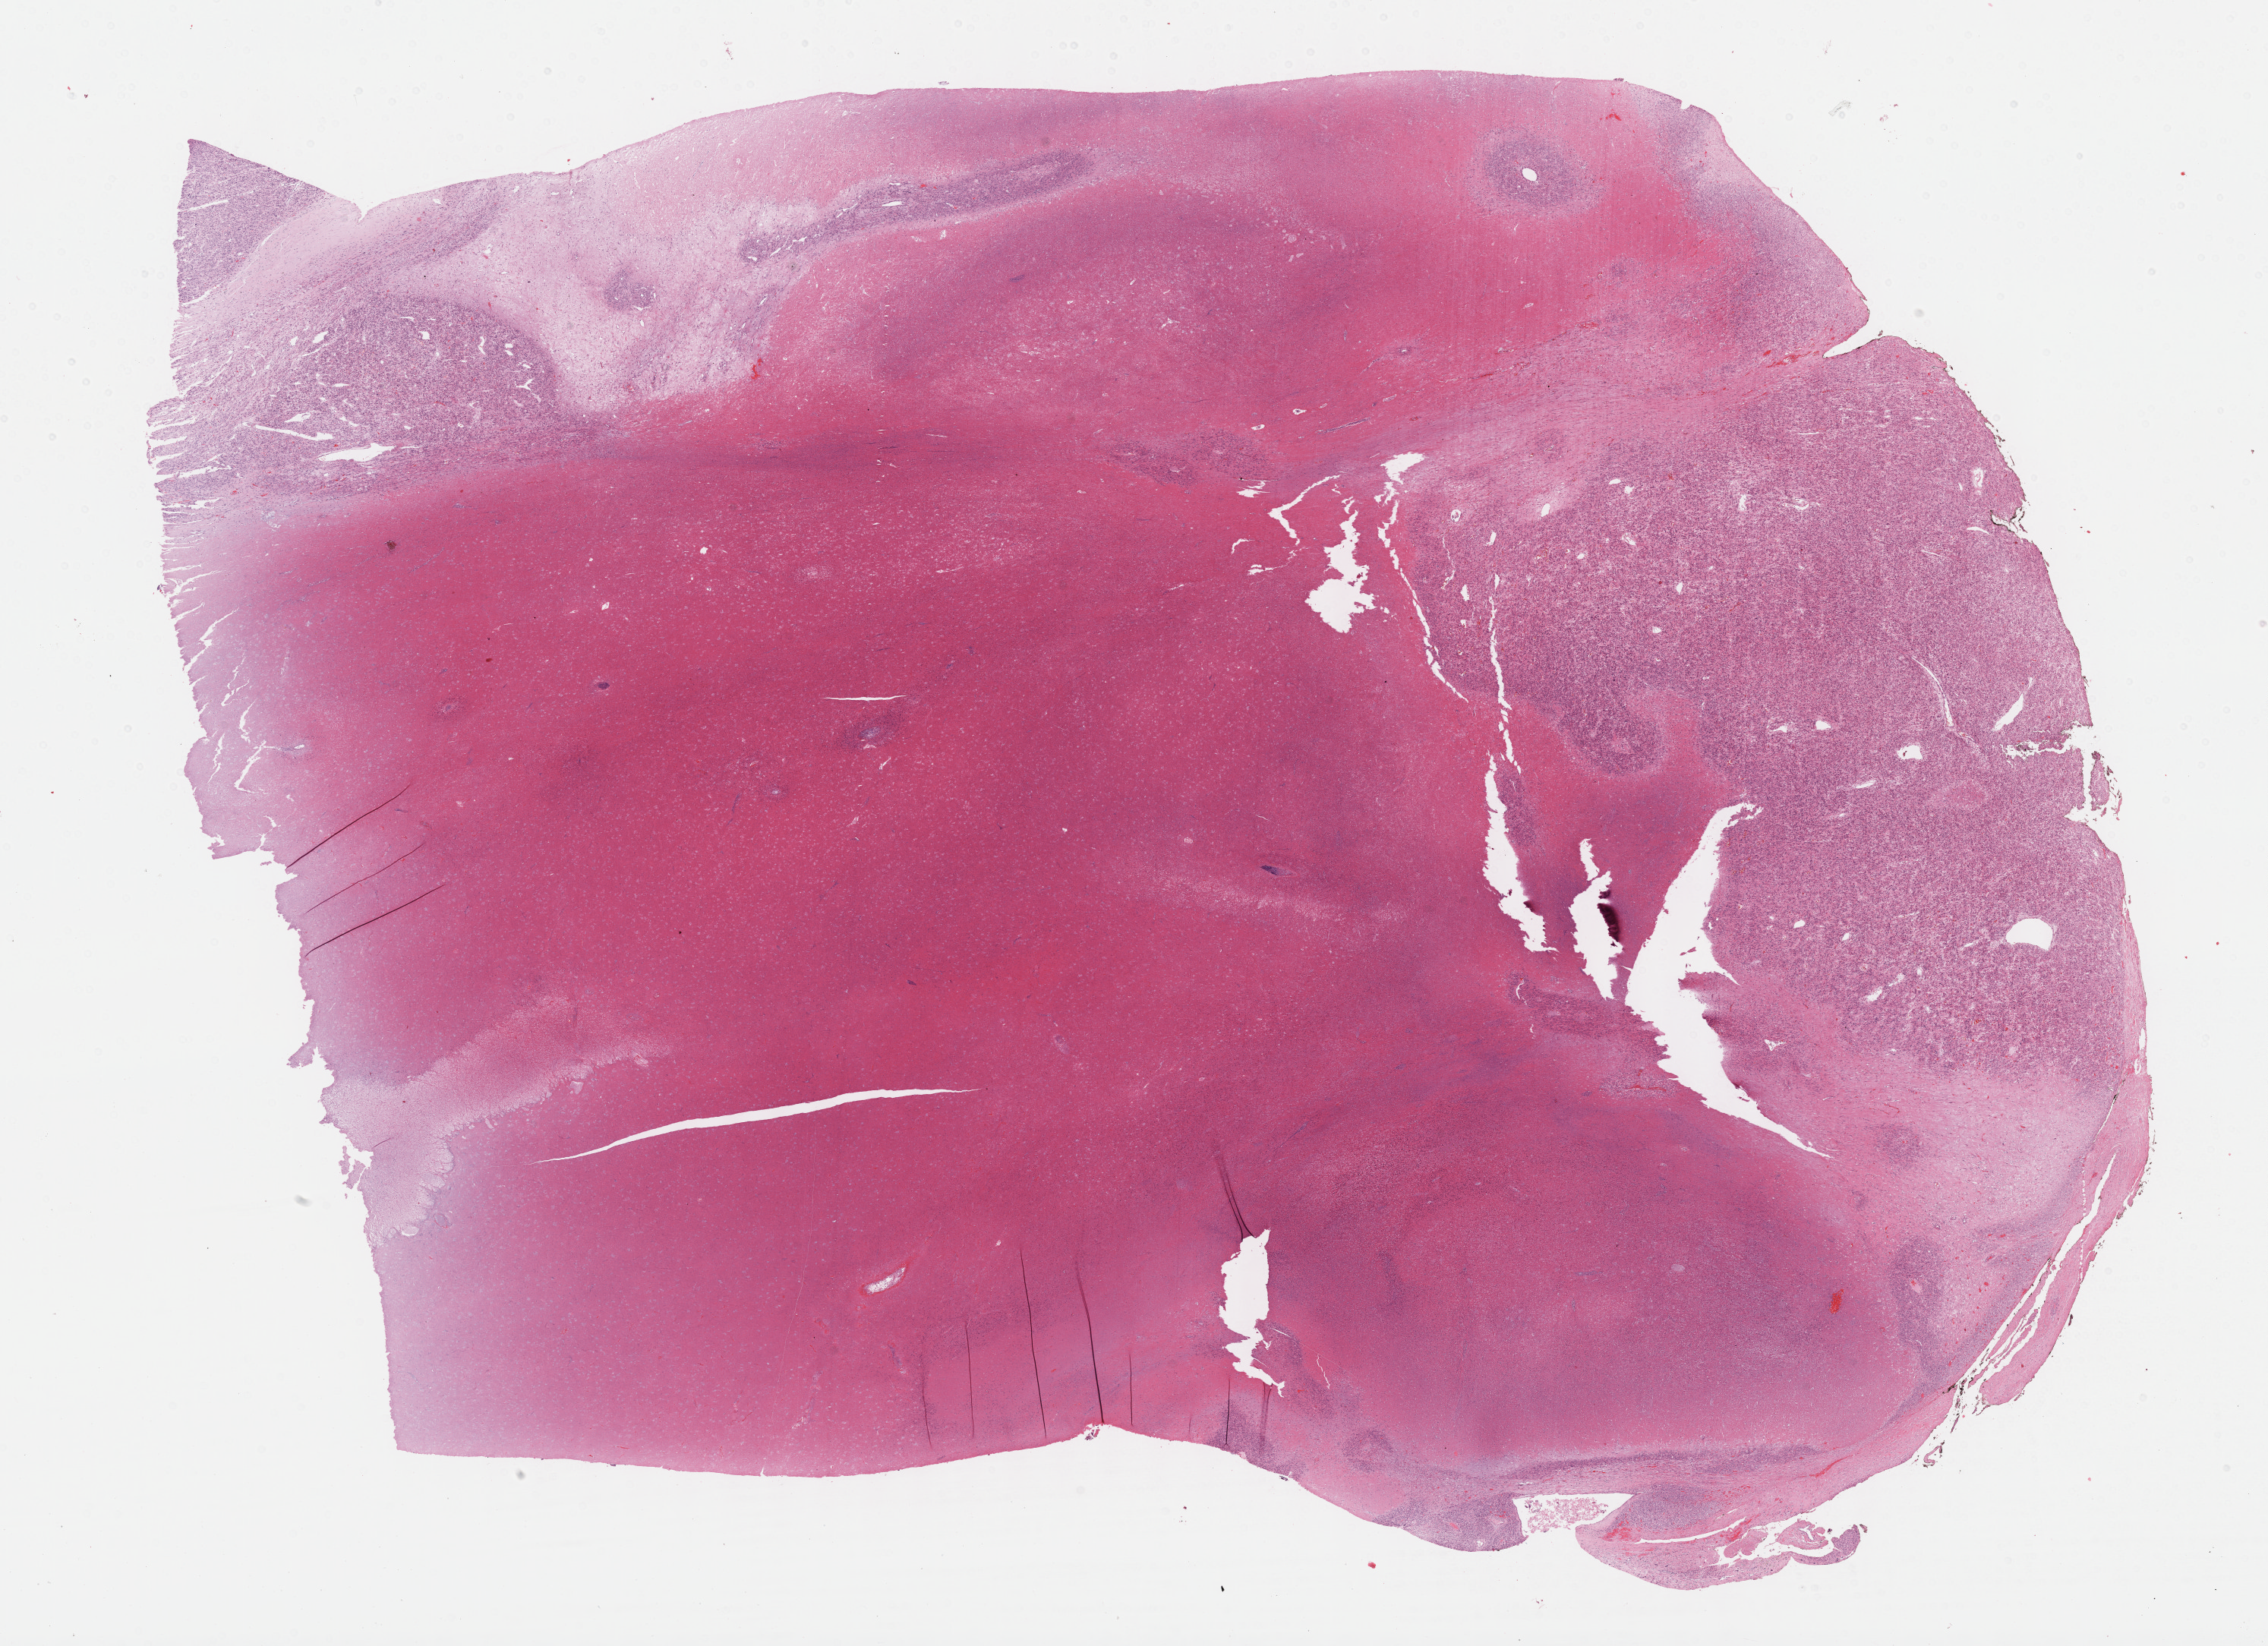
H&E whole-slide image — low-resolution overview of the scanned area, about 24.2 x 17.5 mm. FFPE section. Retroperitoneum and peritoneum, primary tumour sample. Female patient; age at initial diagnosis 53 years.
Pathologic diagnosis: Leiomyosarcoma, NOS (retroperitoneum).